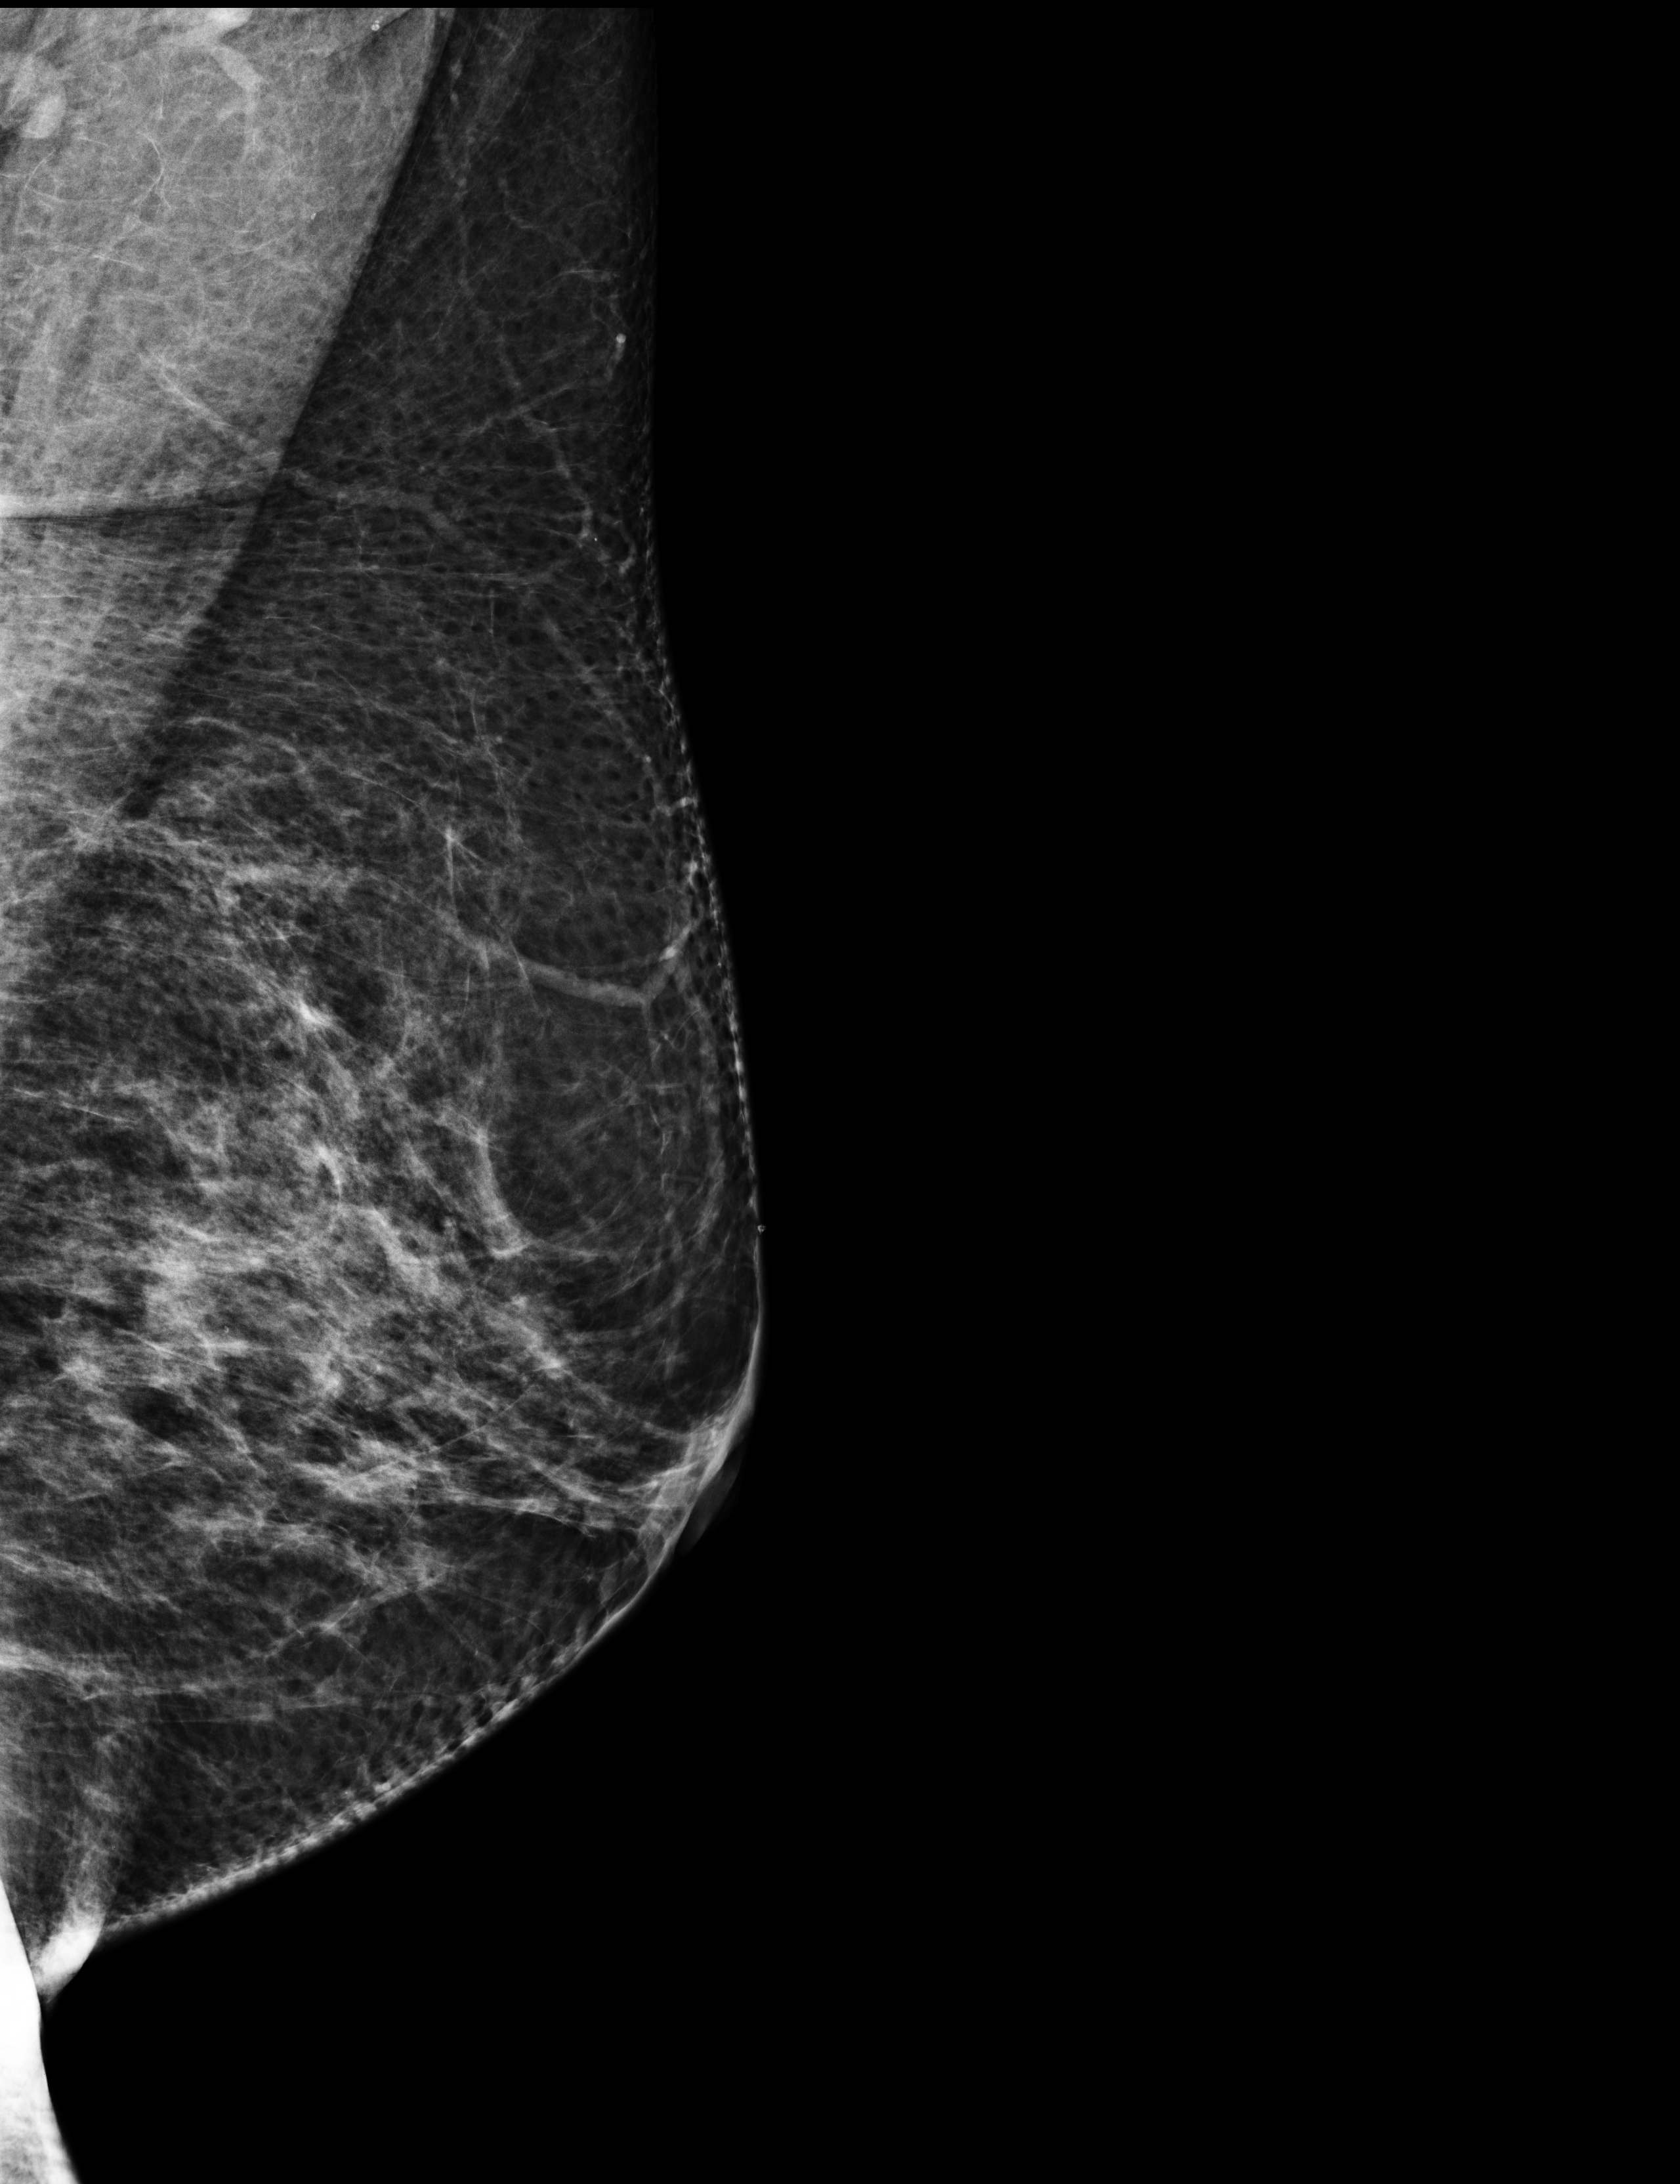
Screening examination.
Image type: full-field digital mammogram. Breast: left. Projection: MLO view.